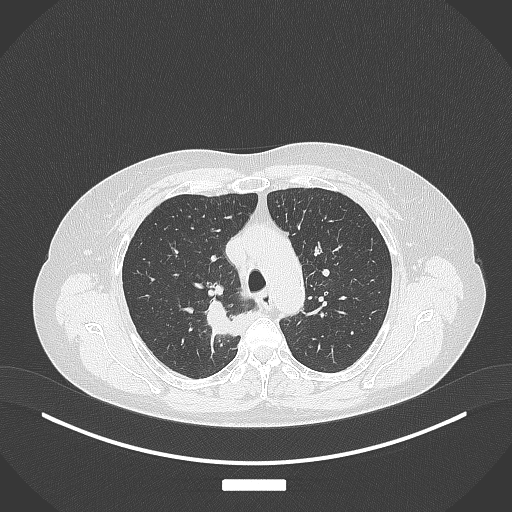
Chest CT, one axial slice; slice 281 of 357 in the series (ordered by position); reconstruction kernel B70f; 120 kVp; lung window (W 1500 / L -600 HU); 1 mm slice thickness; 512 × 512 image matrix, field of view 400 × 400 mm. Female patient, age 62 years. From the clinical record (not read from this slice): clinical TNM (as recorded): T1c N1 M0.
Annotated regions visible in this slice (rectangle marked by the reading radiologist):
- lung tumour (recorded histology: squamous cell carcinoma): bounding box <199,294,253,341> (left, top, right, bottom; pixels)